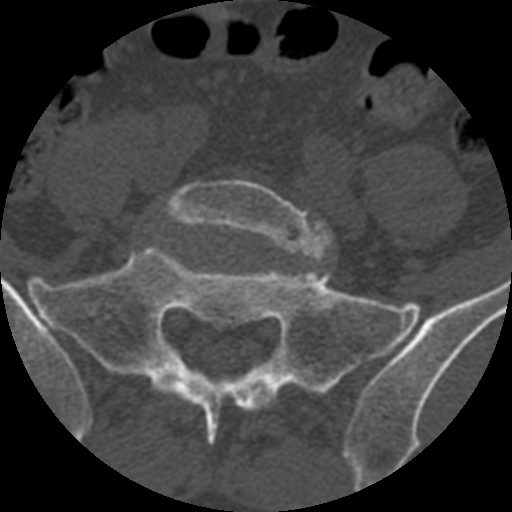
CT including the spine, one axial slice; position 239 of 399 along the scan axis; 120 kVp; bone window (W 1800 / L 400 HU); 1.25 mm slice thickness; 512 × 512 image matrix. Patient age 71 years. From the clinical record (not read from this slice): primary cancer: prostate.
Annotated regions visible in this slice (semi-automatic segmentation, software-assisted and operator-edited):
- L5 vertebra: bounding box [x1, y1, x2, y2] px = [162, 178, 332, 259]